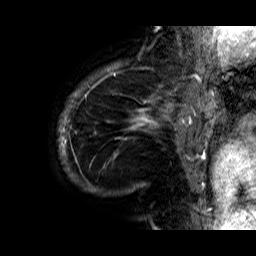
Breast MRI (dynamic contrast-enhanced), one sagittal slice; dynamic contrast-enhanced series, time point 2 of 6 at this slice position (early post-contrast); 1.5 T; TE 6.3 ms, TR 32.9 ms; 4 mm slice thickness; 256 × 256 image matrix. Female patient. Case-level facts recorded for this patient, not image findings: setting: breast cancer imaged before/during neoadjuvant chemotherapy; receptor status: HR-positive, HER2-negative.
Structures marked on this image (semi-automatically segmented with operator editing):
- analysis volume of interest (the breast-tissue region the enhancement analysis was run in; not a lesion): box from (x=58, y=74) to (x=176, y=196) px
- tumour enhancement mask (voxels above the 100 % enhancement threshold inside the analysis volume of interest): (x=58, y=74)–(x=173, y=191)